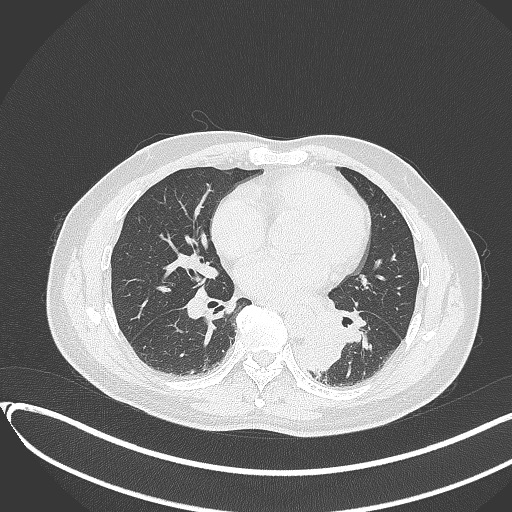
Chest CT, one axial slice; slice 151 of 417 in the series (ordered by position); reconstruction kernel B70f; 120 kVp; lung window (W 1500 / L -600 HU); 512 × 512 image matrix, field of view 400 × 400 mm. Patient: male, 54 years. Case-level facts recorded for this patient, not image findings: clinical TNM (as recorded): T3 N0 M0.
Structures marked on this image (rectangle marked by the reading radiologist):
- lung tumour (recorded histology: squamous cell carcinoma): box from (x=297, y=327) to (x=345, y=379) px